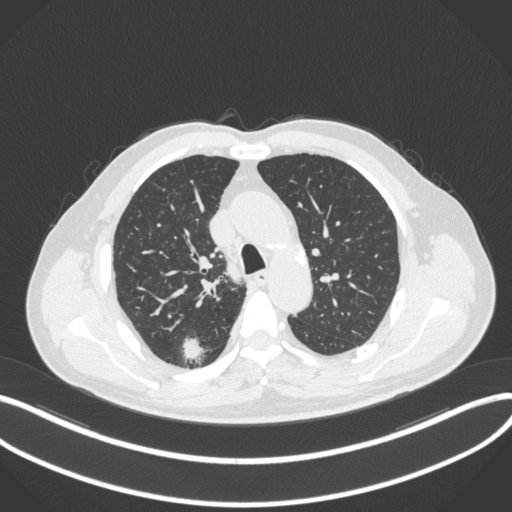
Chest CT, one axial slice; reconstruction kernel B31f; 120 kVp; lung window (W 1500 / L -600 HU); 1 mm slice thickness; 512 × 512 image matrix, field of view 400 × 400 mm. Patient: male, 69 years. From the clinical record (not read from this slice): clinical TNM (as recorded): T1b N0 M0.
Annotated regions visible in this slice (bounding box drawn by a radiologist):
- lung tumour (recorded histology: adenocarcinoma): box from (x=181, y=334) to (x=203, y=362) px